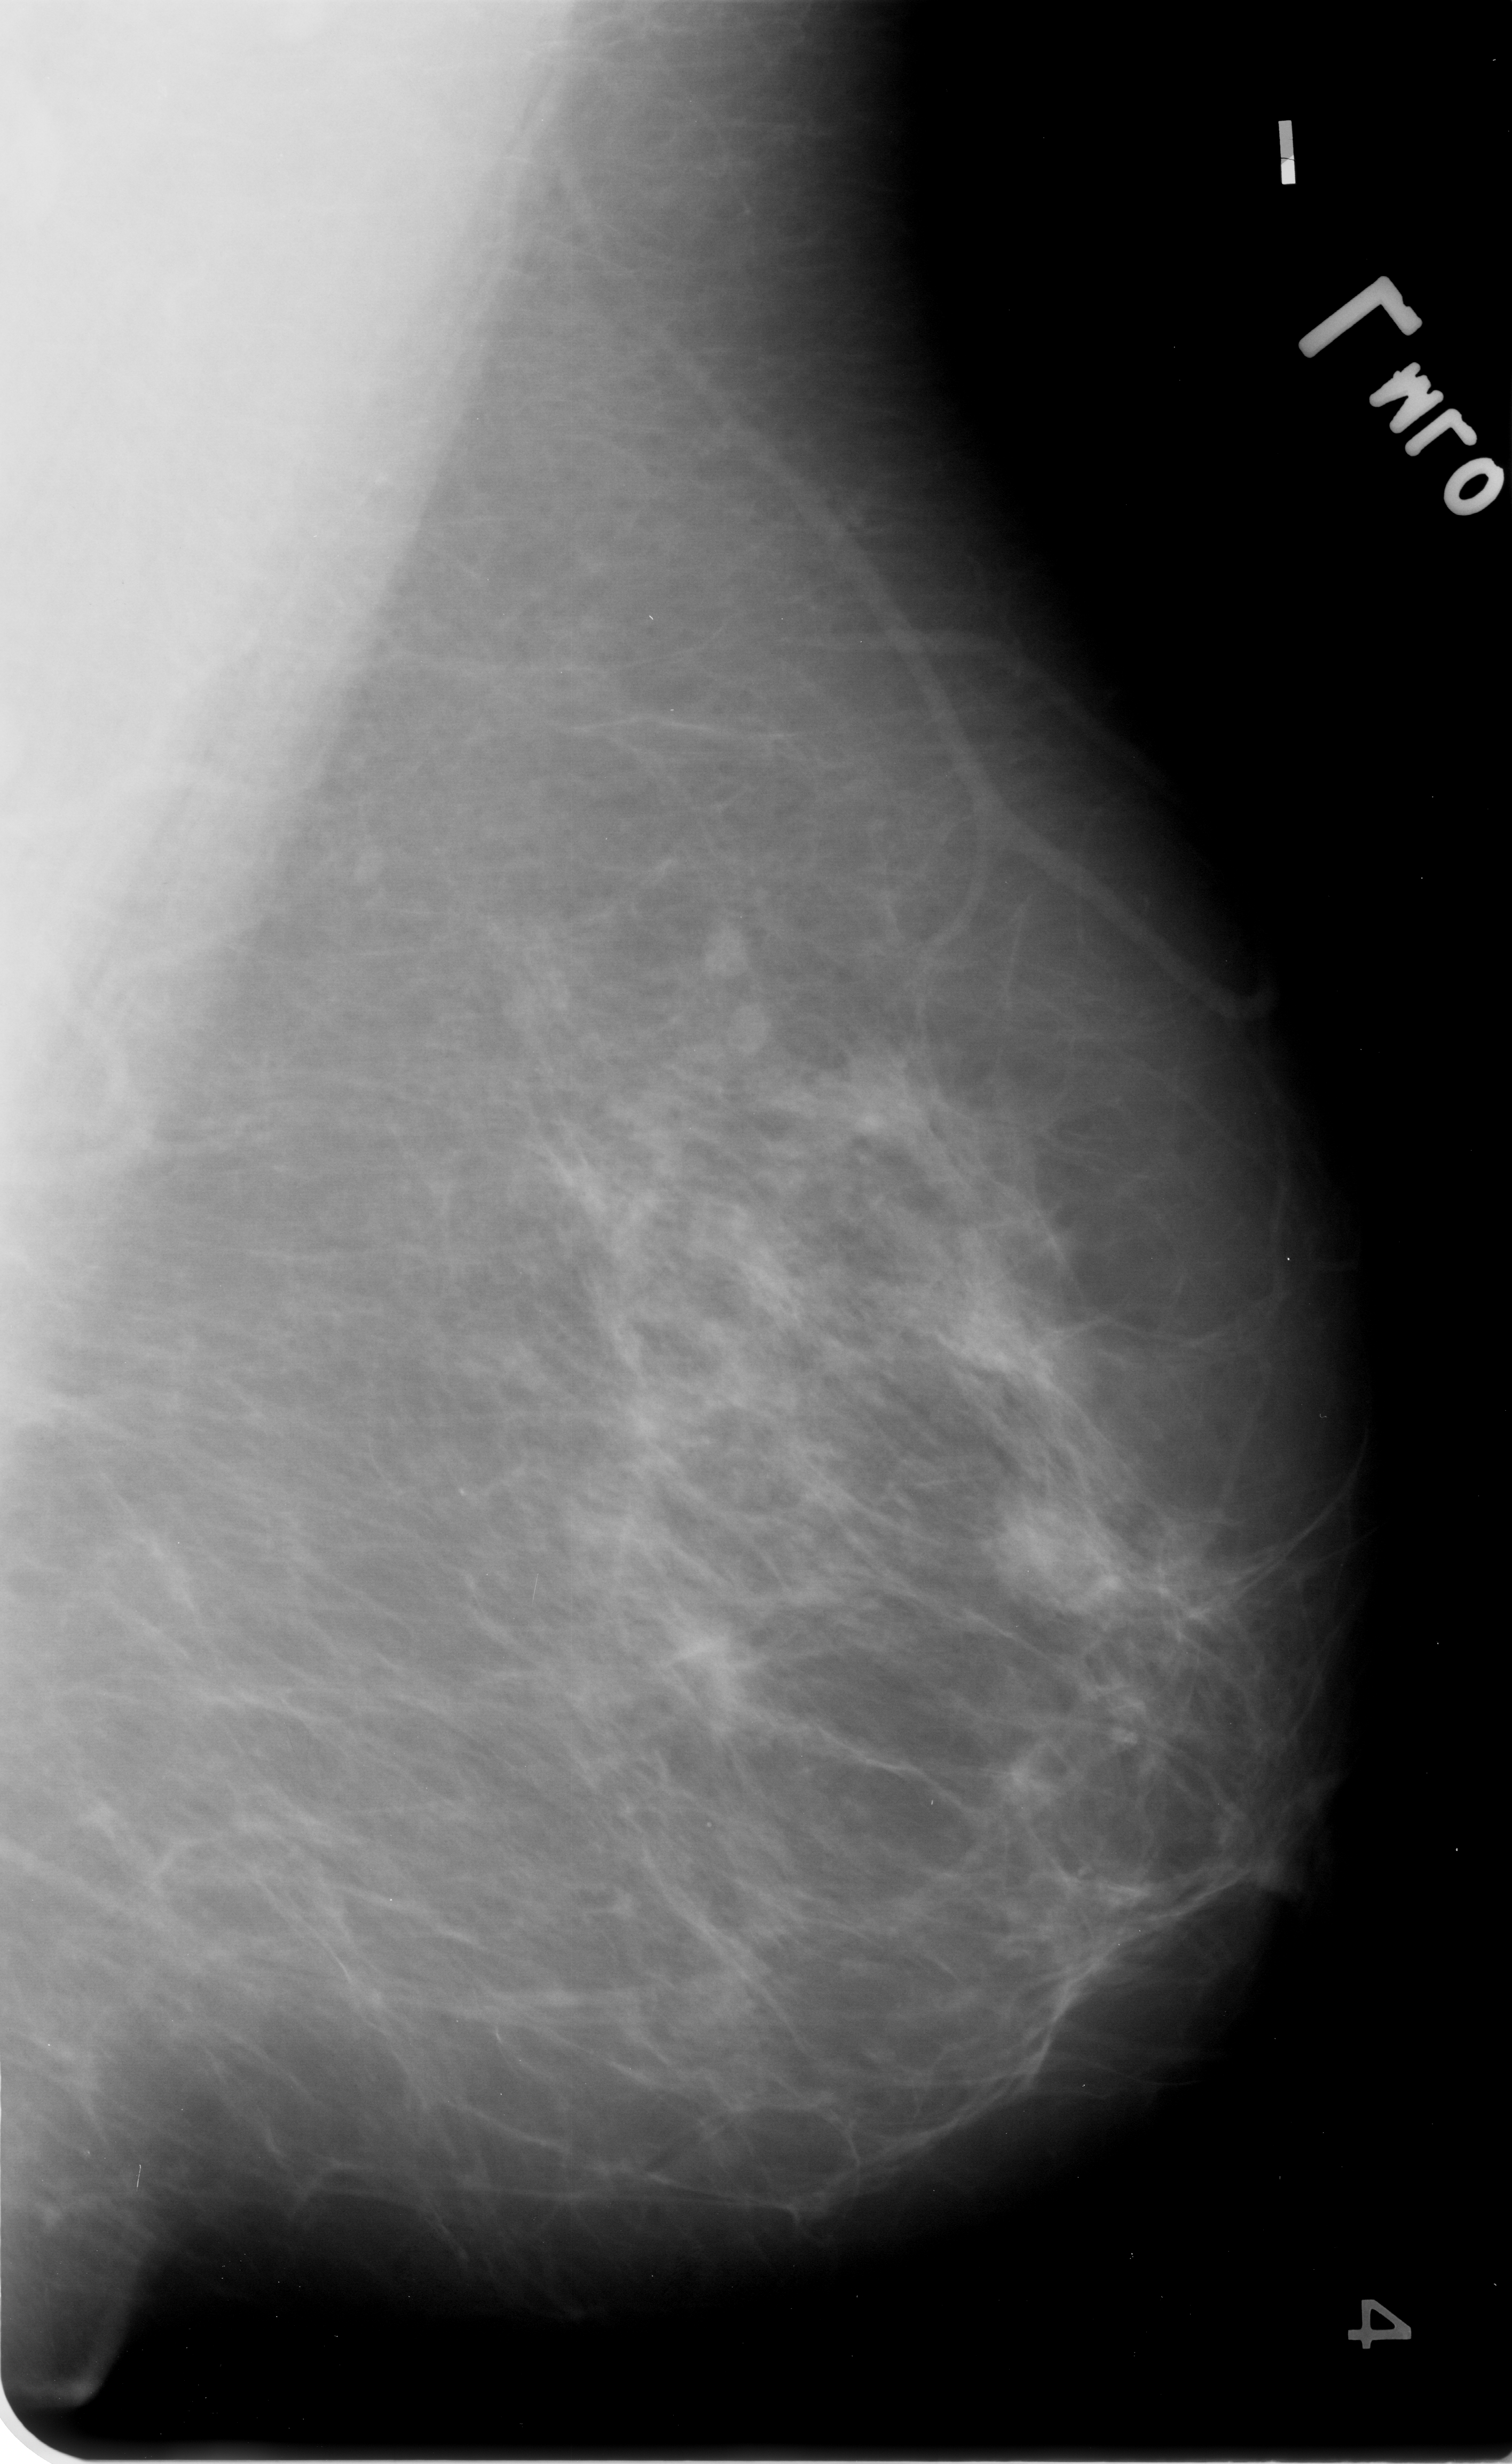
Digitized screen-film mammogram; left breast; MLO view; breast composition: scattered fibroglandular densities (BI-RADS density category 2 of 4); 1512 × 2464 image matrix.
Expert-marked regions of interest on this film, with their recorded descriptors:
- mass, shape oval, margins obscured / ill defined; BI-RADS assessment category 3; pathology result (as recorded, not read from the image): malignant: bounding box [x1, y1, x2, y2] px = [983, 1498, 1133, 1621]